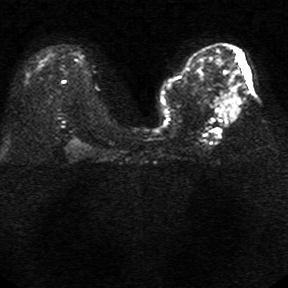
Breast MRI, one axial slice; diffusion-weighted series; image 2 of 4 stored at this slice position (different b-values; order by instance number); 1.5 T; 288 × 288 image matrix, field of view 340 × 340 mm. Female patient.
Outlined on this slice (outlined manually by an expert reader):
- tumour on diffusion-weighted imaging: bounding box (x1, y1, x2, y2) in pixels: (218, 93, 241, 120)